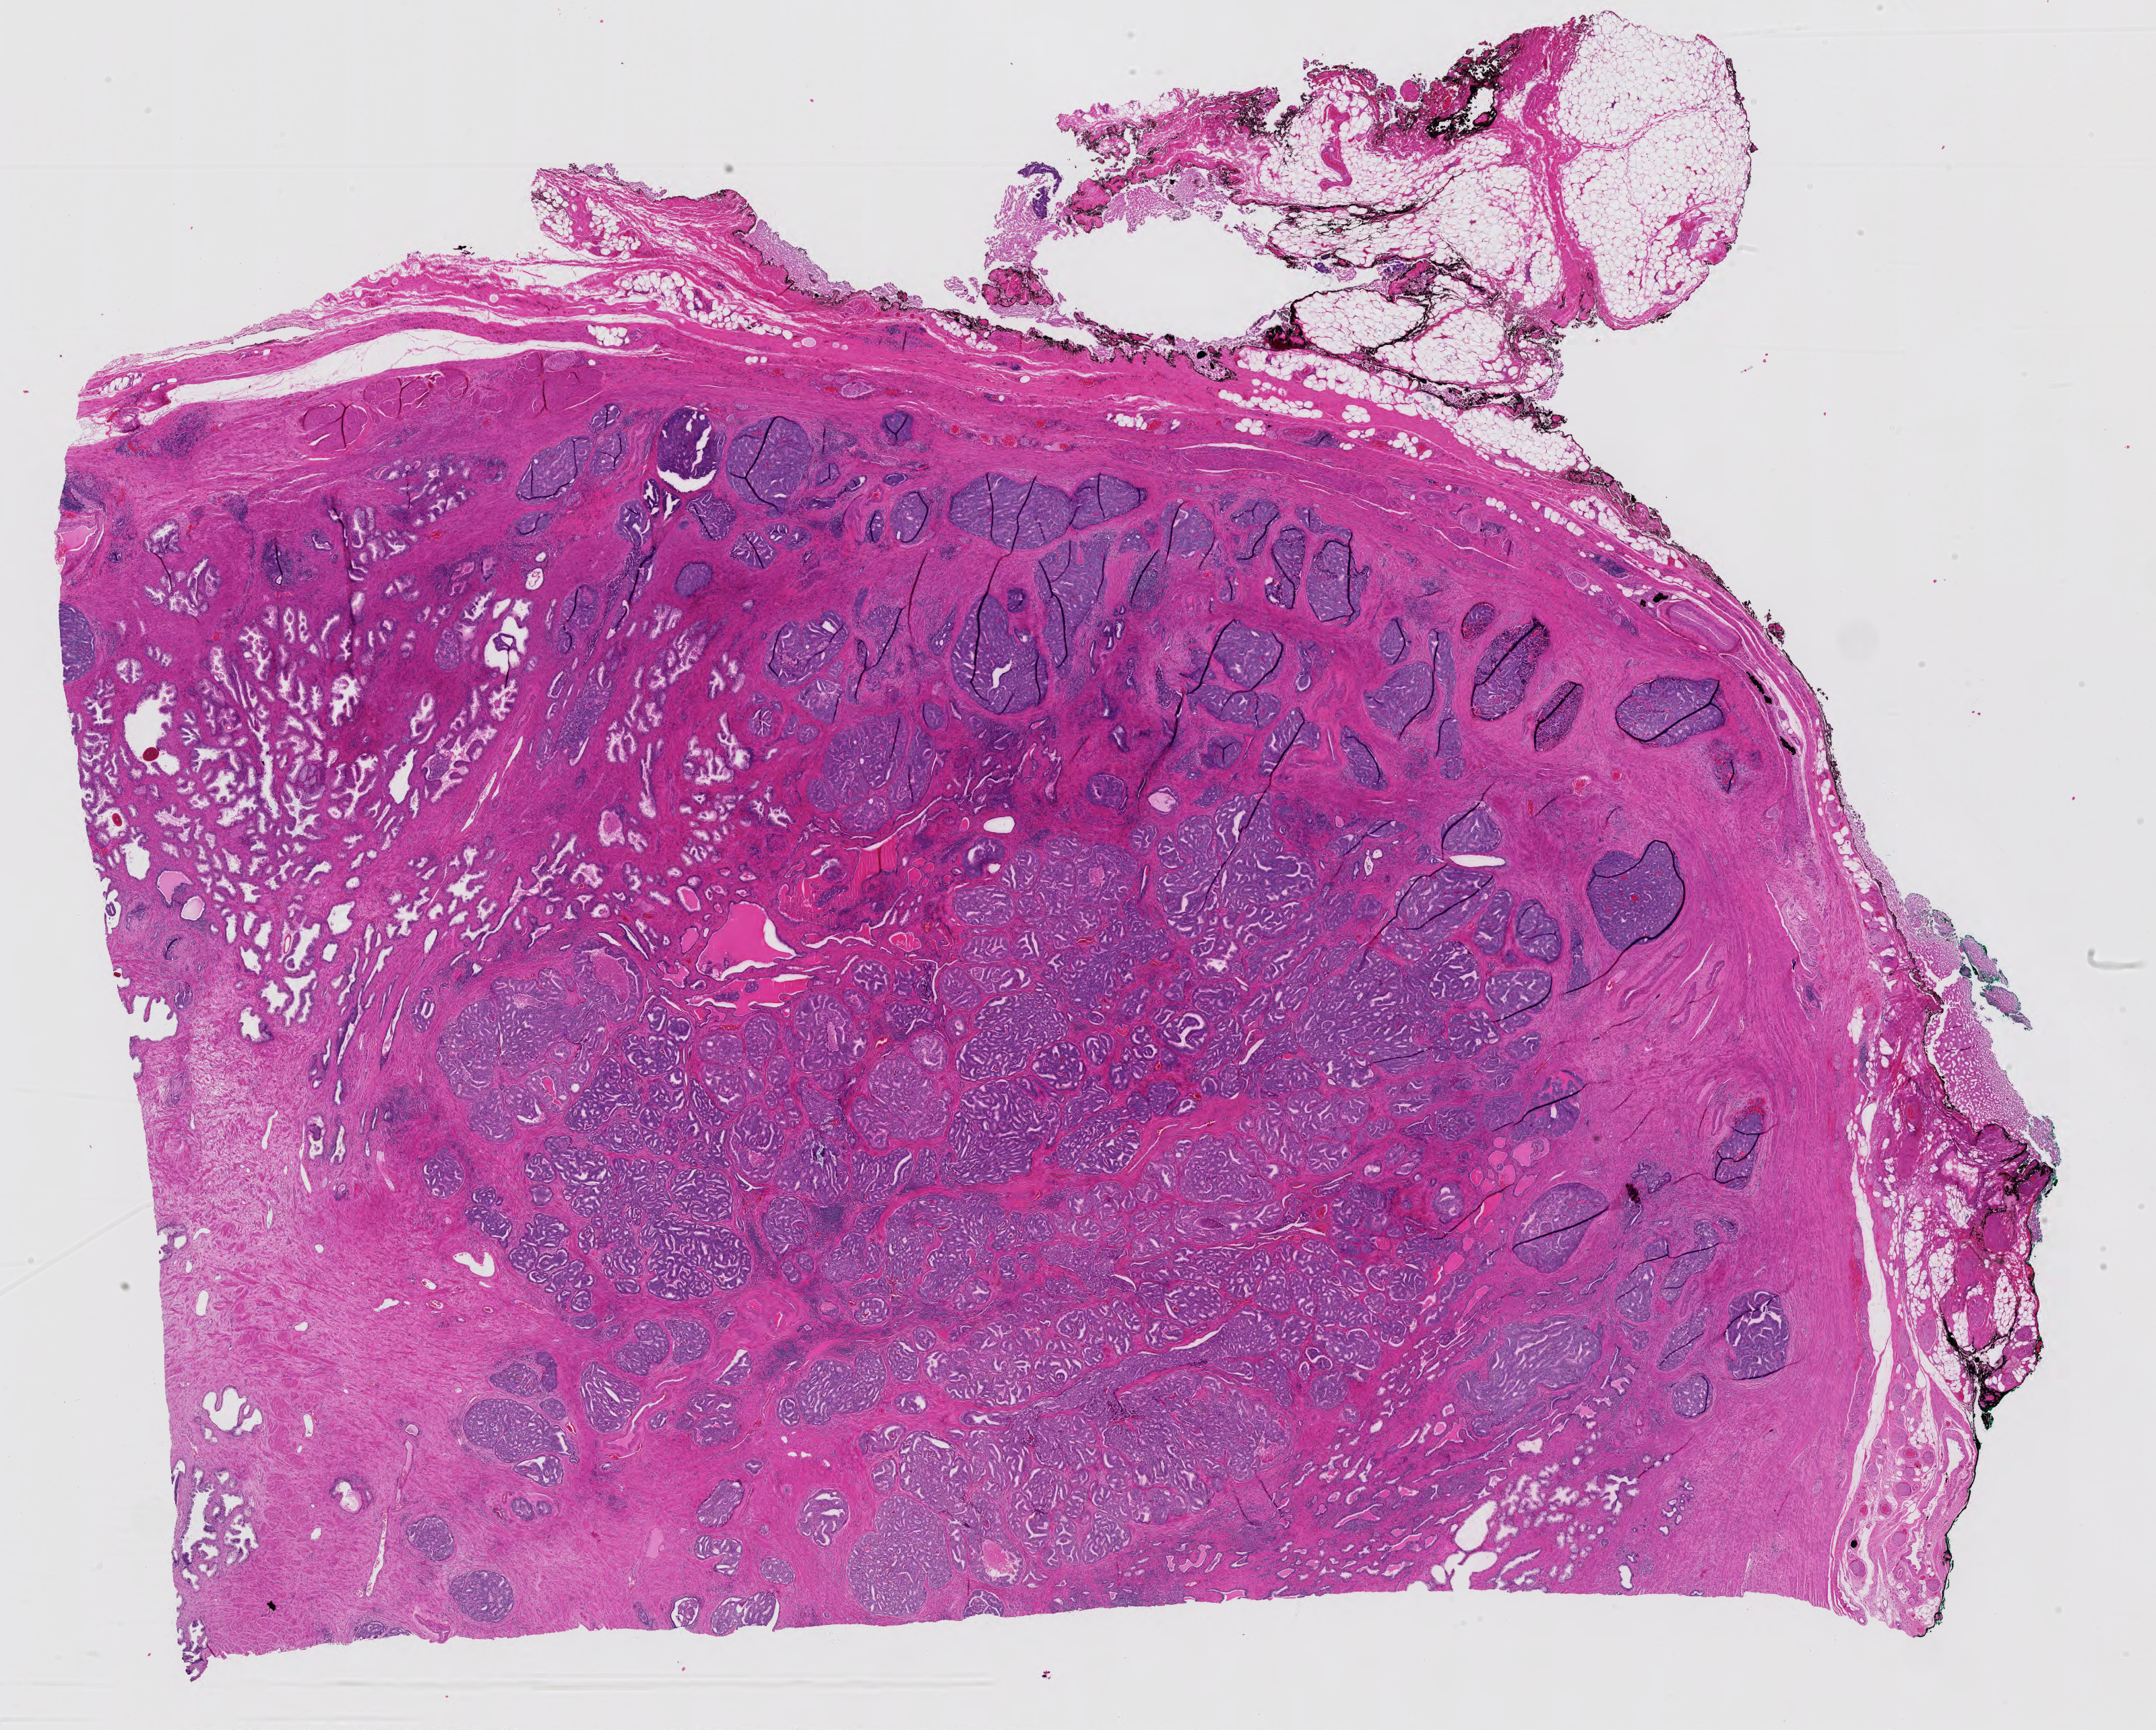
Digitized H&E-stained tissue section (whole slide), shown as a low-resolution overview of the whole scanned area (about 23.2 x 18.6 mm). FFPE section. Sample: primary tumour, prostate. Male, age 74 years at initial diagnosis. Gleason score: 8 (4+4).
Laterality: bilateral. Histologic diagnosis: Adenocarcinoma, NOS (prostate gland). Lymph nodes positive (case pathology): 3 of 19 examined.